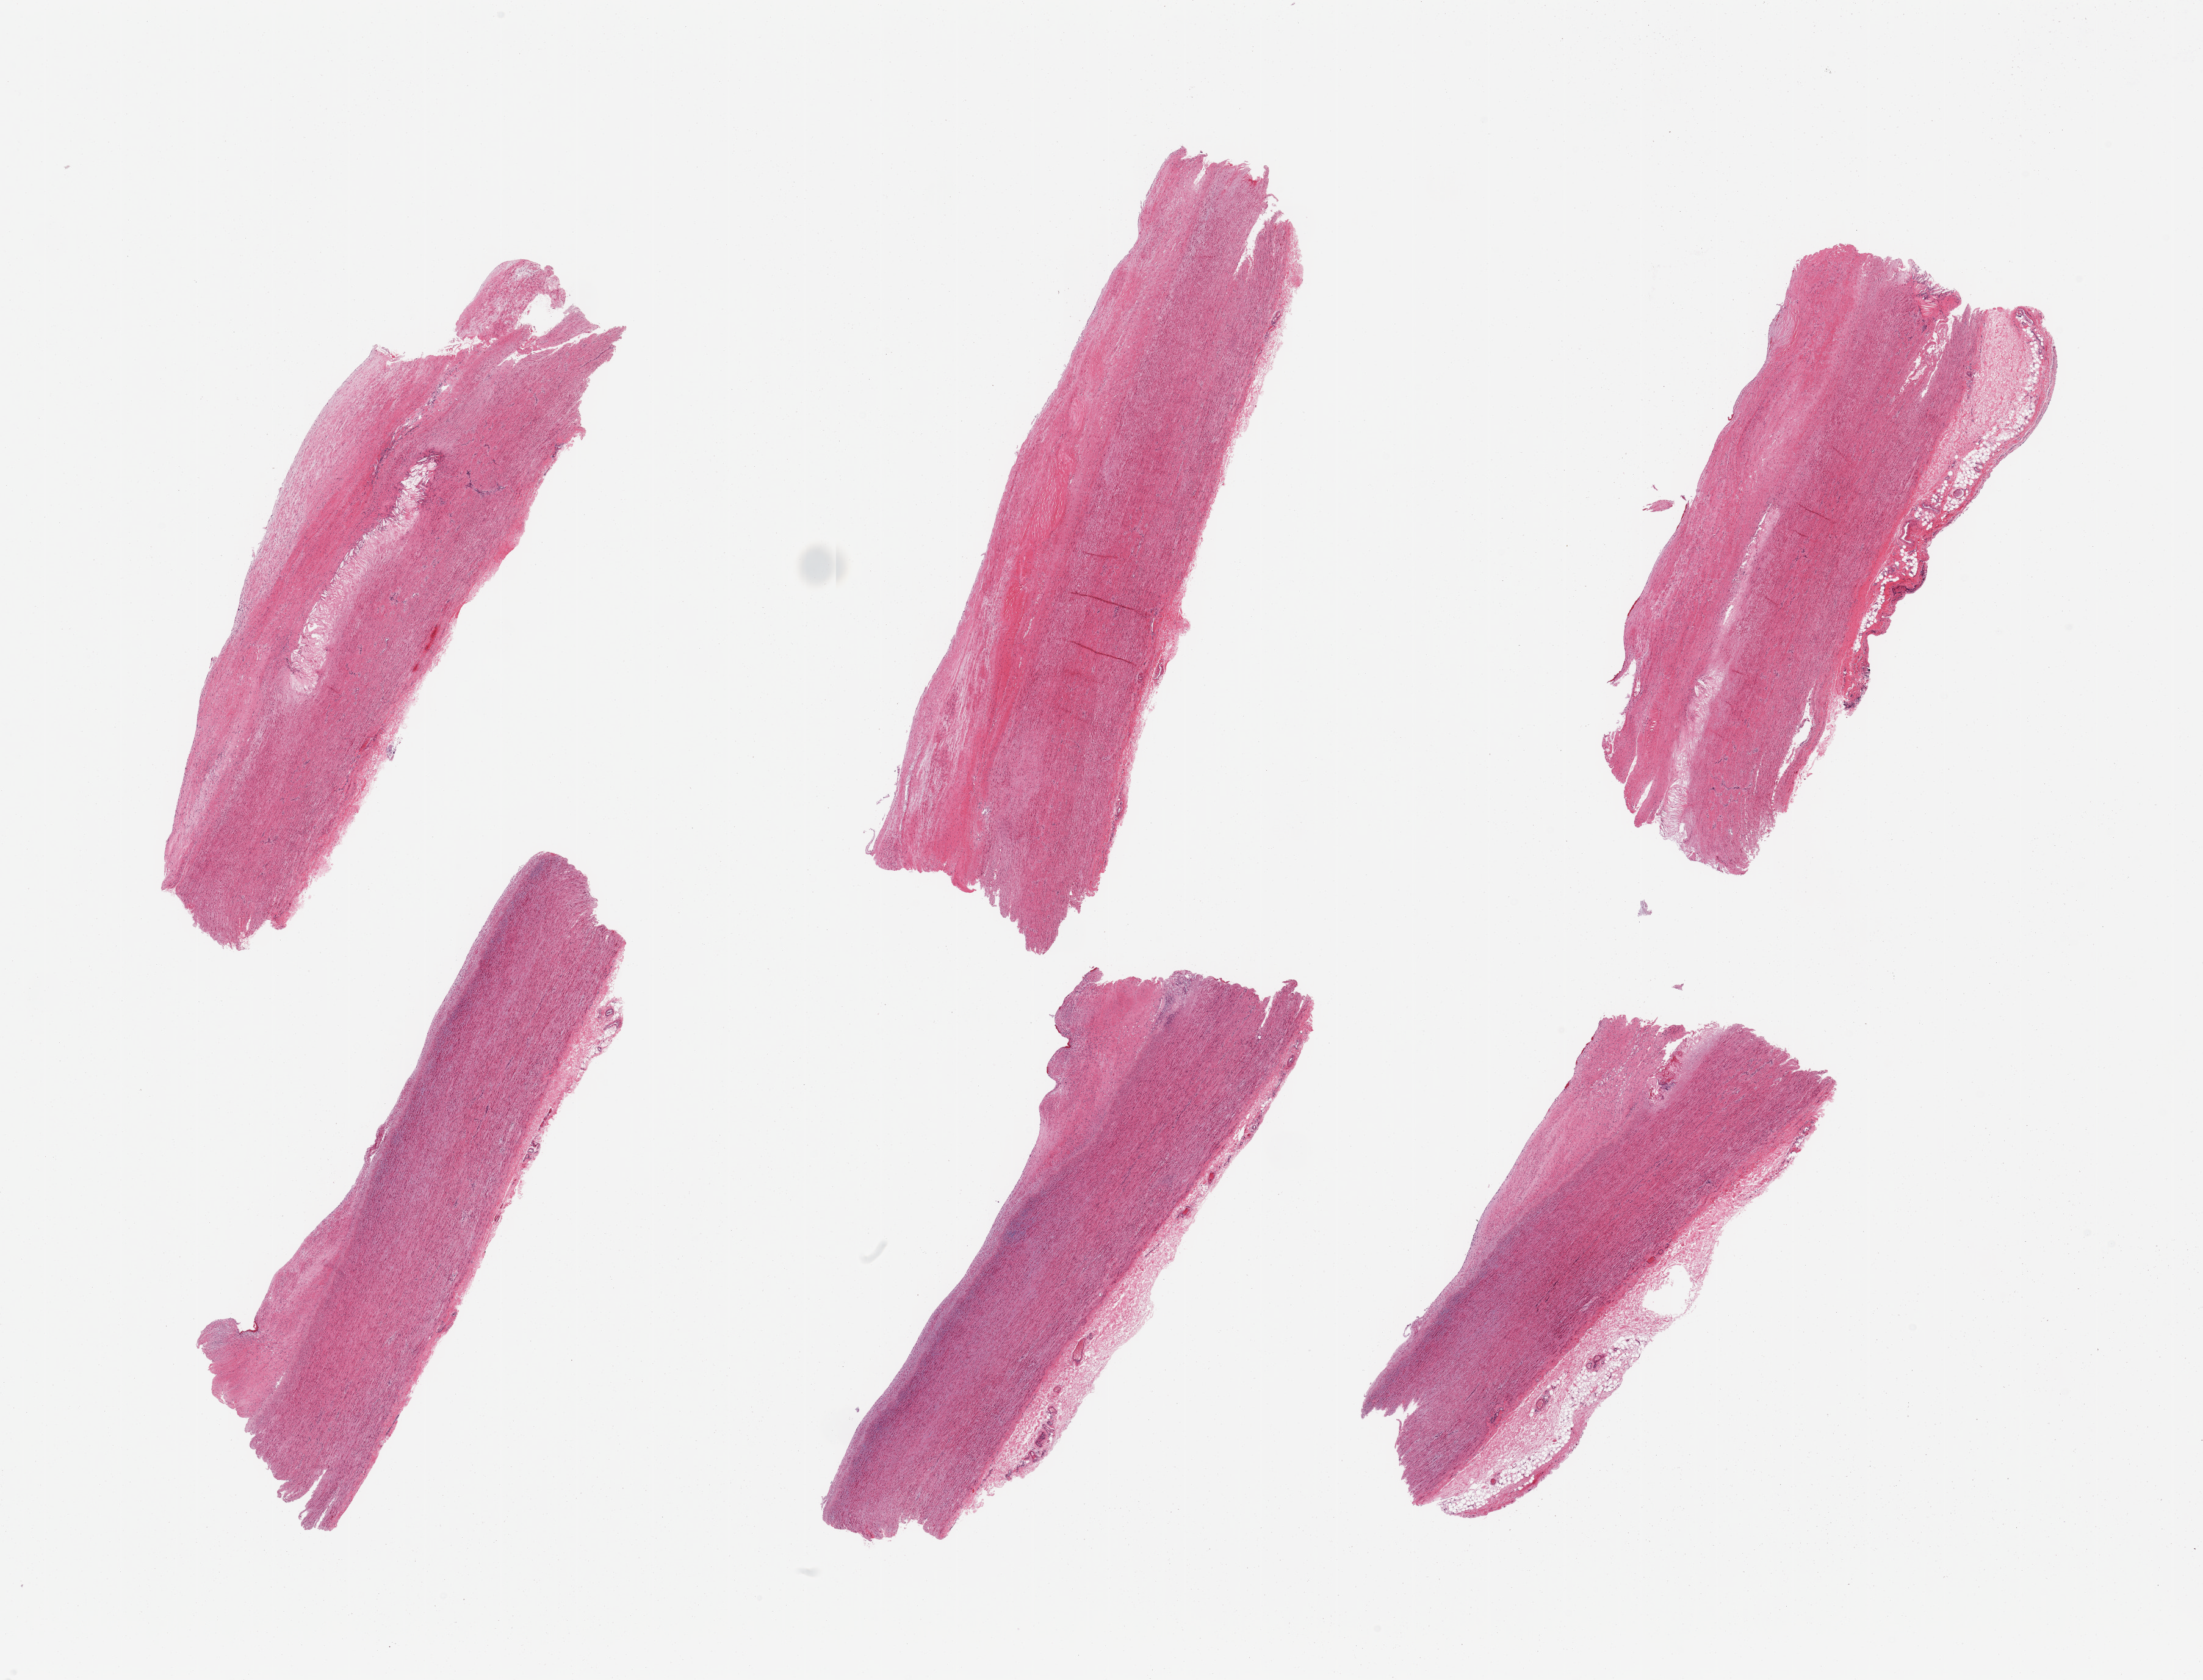
Whole-slide image, haematoxylin and eosin stain — low-resolution overview of the scanned area, about 28.5 x 21.8 mm (from a 20x scan); PAXgene-fixed, paraffin-embedded tissue; section of aorta (target tissue); donor tissue sample. Donor sex: male.
- reviewer comment on this tissue sample: 6 pieces; moderate fibroatheromatous plaques